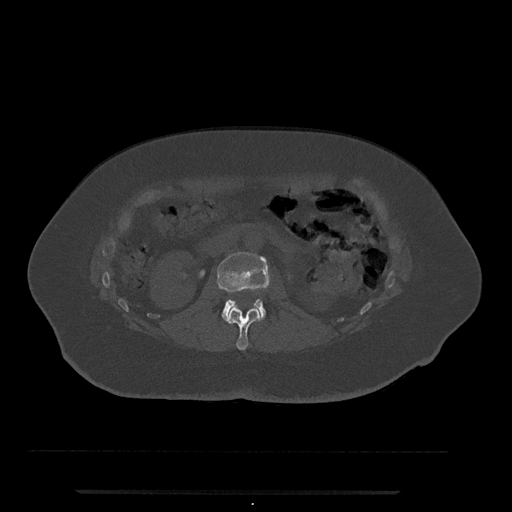
CT including the spine, one axial slice. Position 67 of 797 along the scan axis. 120 kVp. Bone window (W 1800 / L 400 HU). 0.5 mm slice thickness. 512 × 512 image matrix, field of view 440 × 440 mm. Female patient, age 51 years. Case-level facts recorded for this patient, not image findings: primary cancer: neuro; vertebrae with lytic lesions (as recorded): T8.
Structures marked on this image (semi-automatically segmented with operator editing):
- L1 vertebra: bounding box (x1, y1, x2, y2) in pixels: (225, 307, 262, 350)
- L2 vertebra: (217, 252, 270, 321)